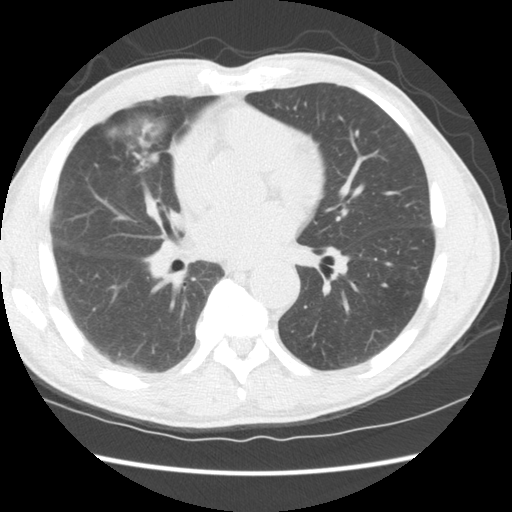
Low-dose screening chest CT, one axial slice. Slice 68 of 147 in the series (ordered by position). Reconstruction kernel STANDARD. 120 kVp. Lung window (W 1500 / L -600 HU). 512 × 512 image matrix, field of view 345 × 345 mm.
Annotated regions visible in this slice (manually delineated by an expert):
- lesion 1 (tumor, middle lobe of right lung): box from (x=151, y=154) to (x=157, y=161) px